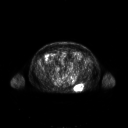
FDG PET of an extremity soft-tissue mass (from a PET/CT study), one axial slice; position 84 of 267 along the scan axis; 128 × 128 image matrix, field of view 700 × 700 mm. Patient: male, 61 years. Case-level facts recorded for this patient, not image findings: histological type: pleiomorphic leiomyosarcoma; grade: high; site of the primary tumour: left buttock.
Structures marked on this image (expert contour drawn on MRI and transferred to this co-registered scan by the dataset authors):
- gross tumour volume including surrounding oedema: bounding box [x1, y1, x2, y2] px = [74, 84, 84, 91]
- gross tumour volume (mass): [74, 84, 83, 91]